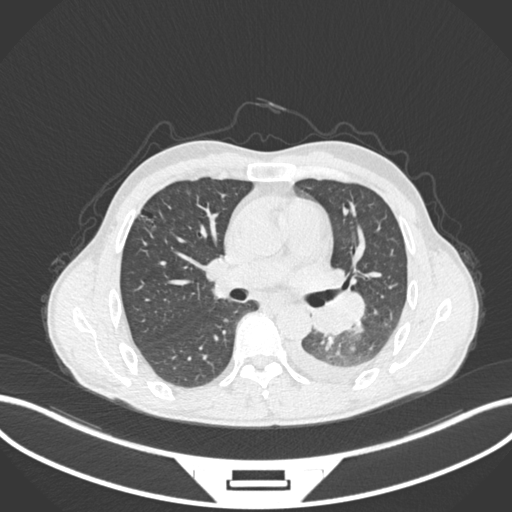
Chest CT, one axial slice; position 138 of 222 along the scan axis; 120 kVp; lung window (W 1500 / L -600 HU); 1 mm slice thickness; 512 × 512 image matrix. Male patient, age 47 years. From the clinical record (not read from this slice): clinical TNM (as recorded): T3 N1 M1c.
Structures marked on this image (bounding box drawn by a radiologist):
- lung tumour (recorded histology: small cell carcinoma): bounding box (x1, y1, x2, y2) in pixels: (308, 287, 366, 340)